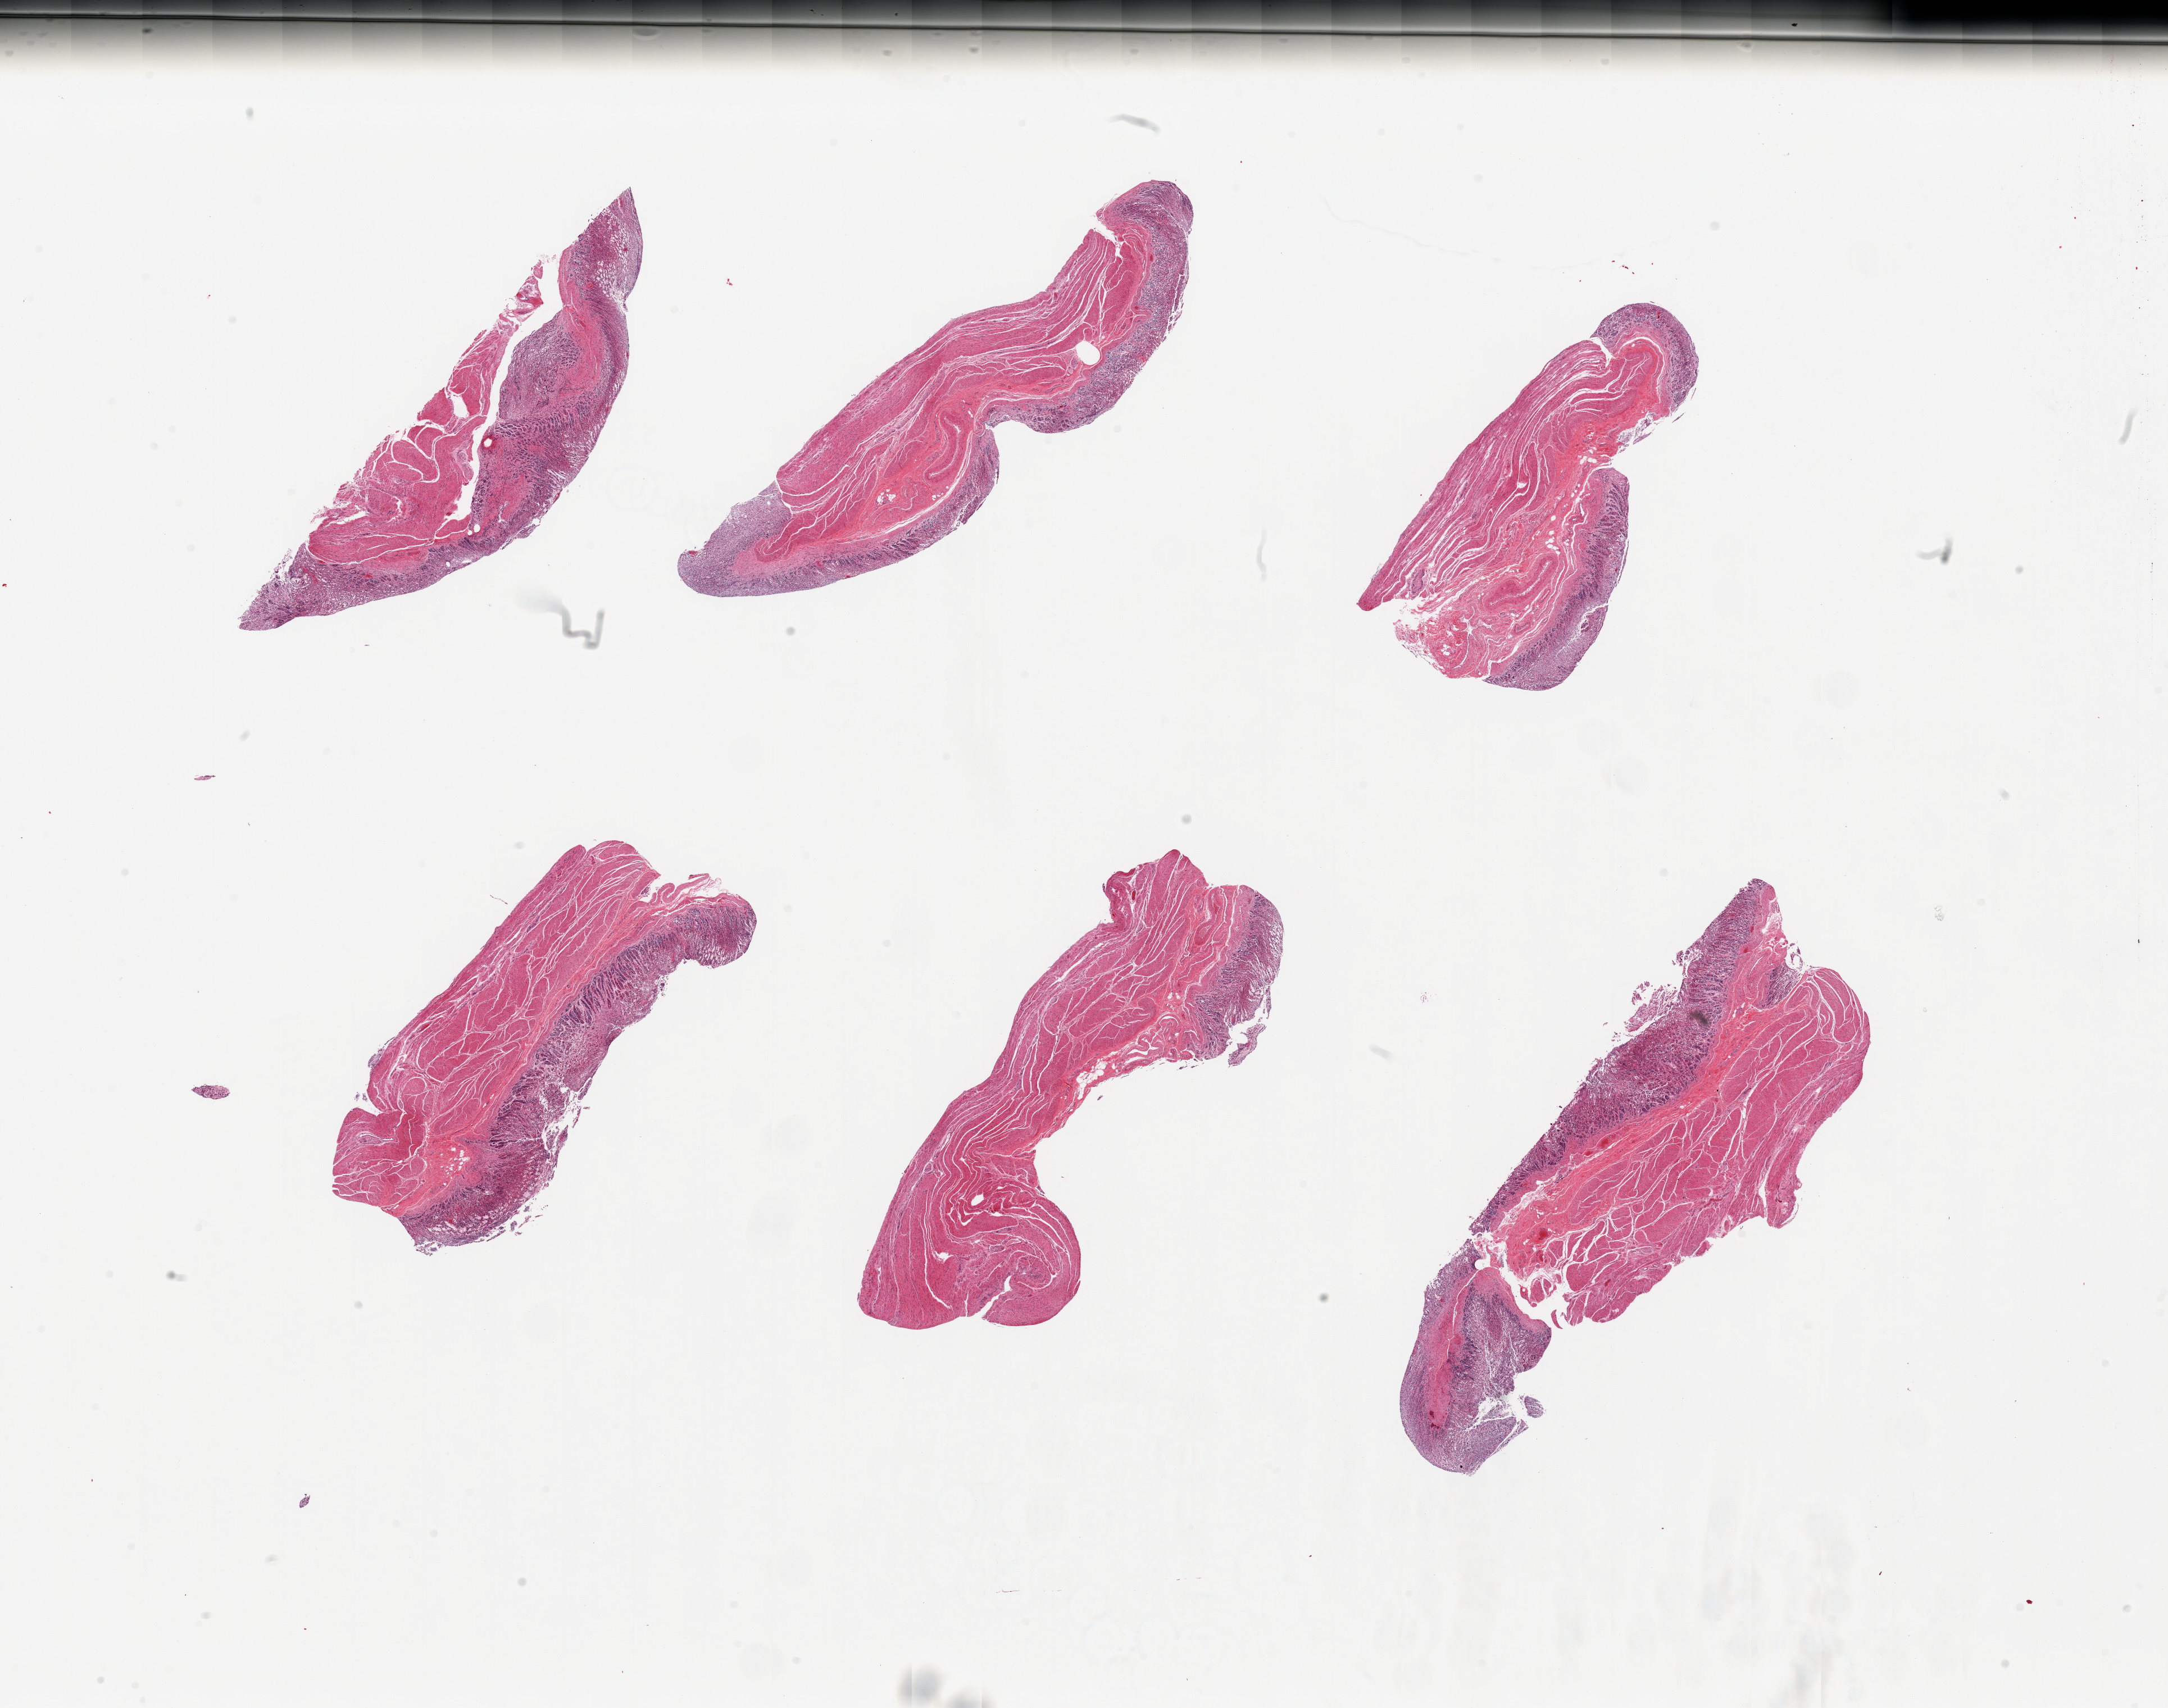
Digitized haematoxylin and eosin-stained section, a low-resolution overview of the entire scanned area, about 30.5 x 24.0 mm. PAXgene-fixed paraffin-embedded (PFPE) section. Section of stomach (target tissue). Donor tissue sample. Donor sex: male.
* pathologist's review note for this sample: 6 pieces; full thickness sections, moderate to severe autolysis of mucosa